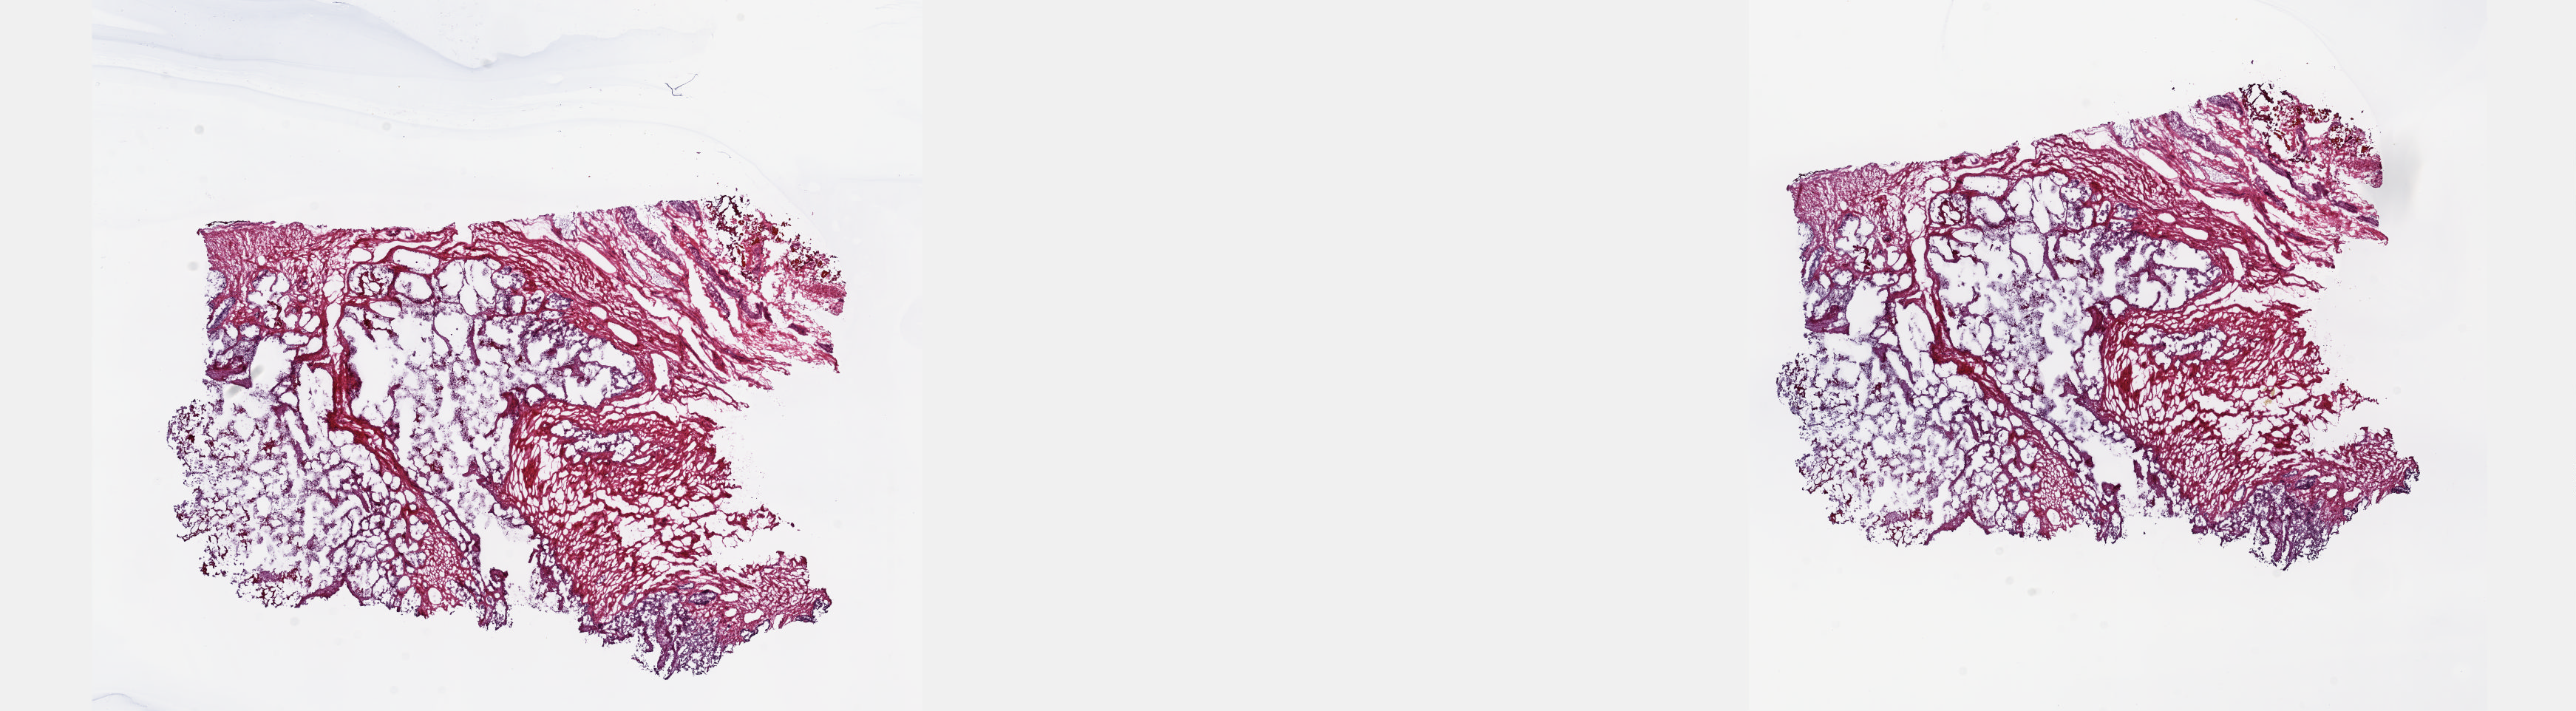
H&E-stained whole-slide image, shown as a low-resolution overview of the whole scanned area (about 28.1 x 7.8 mm); frozen section from the top of the tissue portion; solid tissue normal (non-tumour tissue) sample from the prostate. Male, age 69 years at initial diagnosis. Composition of this section per pathologist review: tumour cells 0%, tumour nuclei 0%, normal cells 50%, stromal cells 50%, necrosis 0%. Infiltration values recorded for this section: lymphocyte infiltration 40%, monocyte infiltration 20%, neutrophil infiltration 20%.
This section: solid tissue normal sample (biorepository sample class). Patient diagnosis: Adenocarcinoma, NOS (prostate gland).